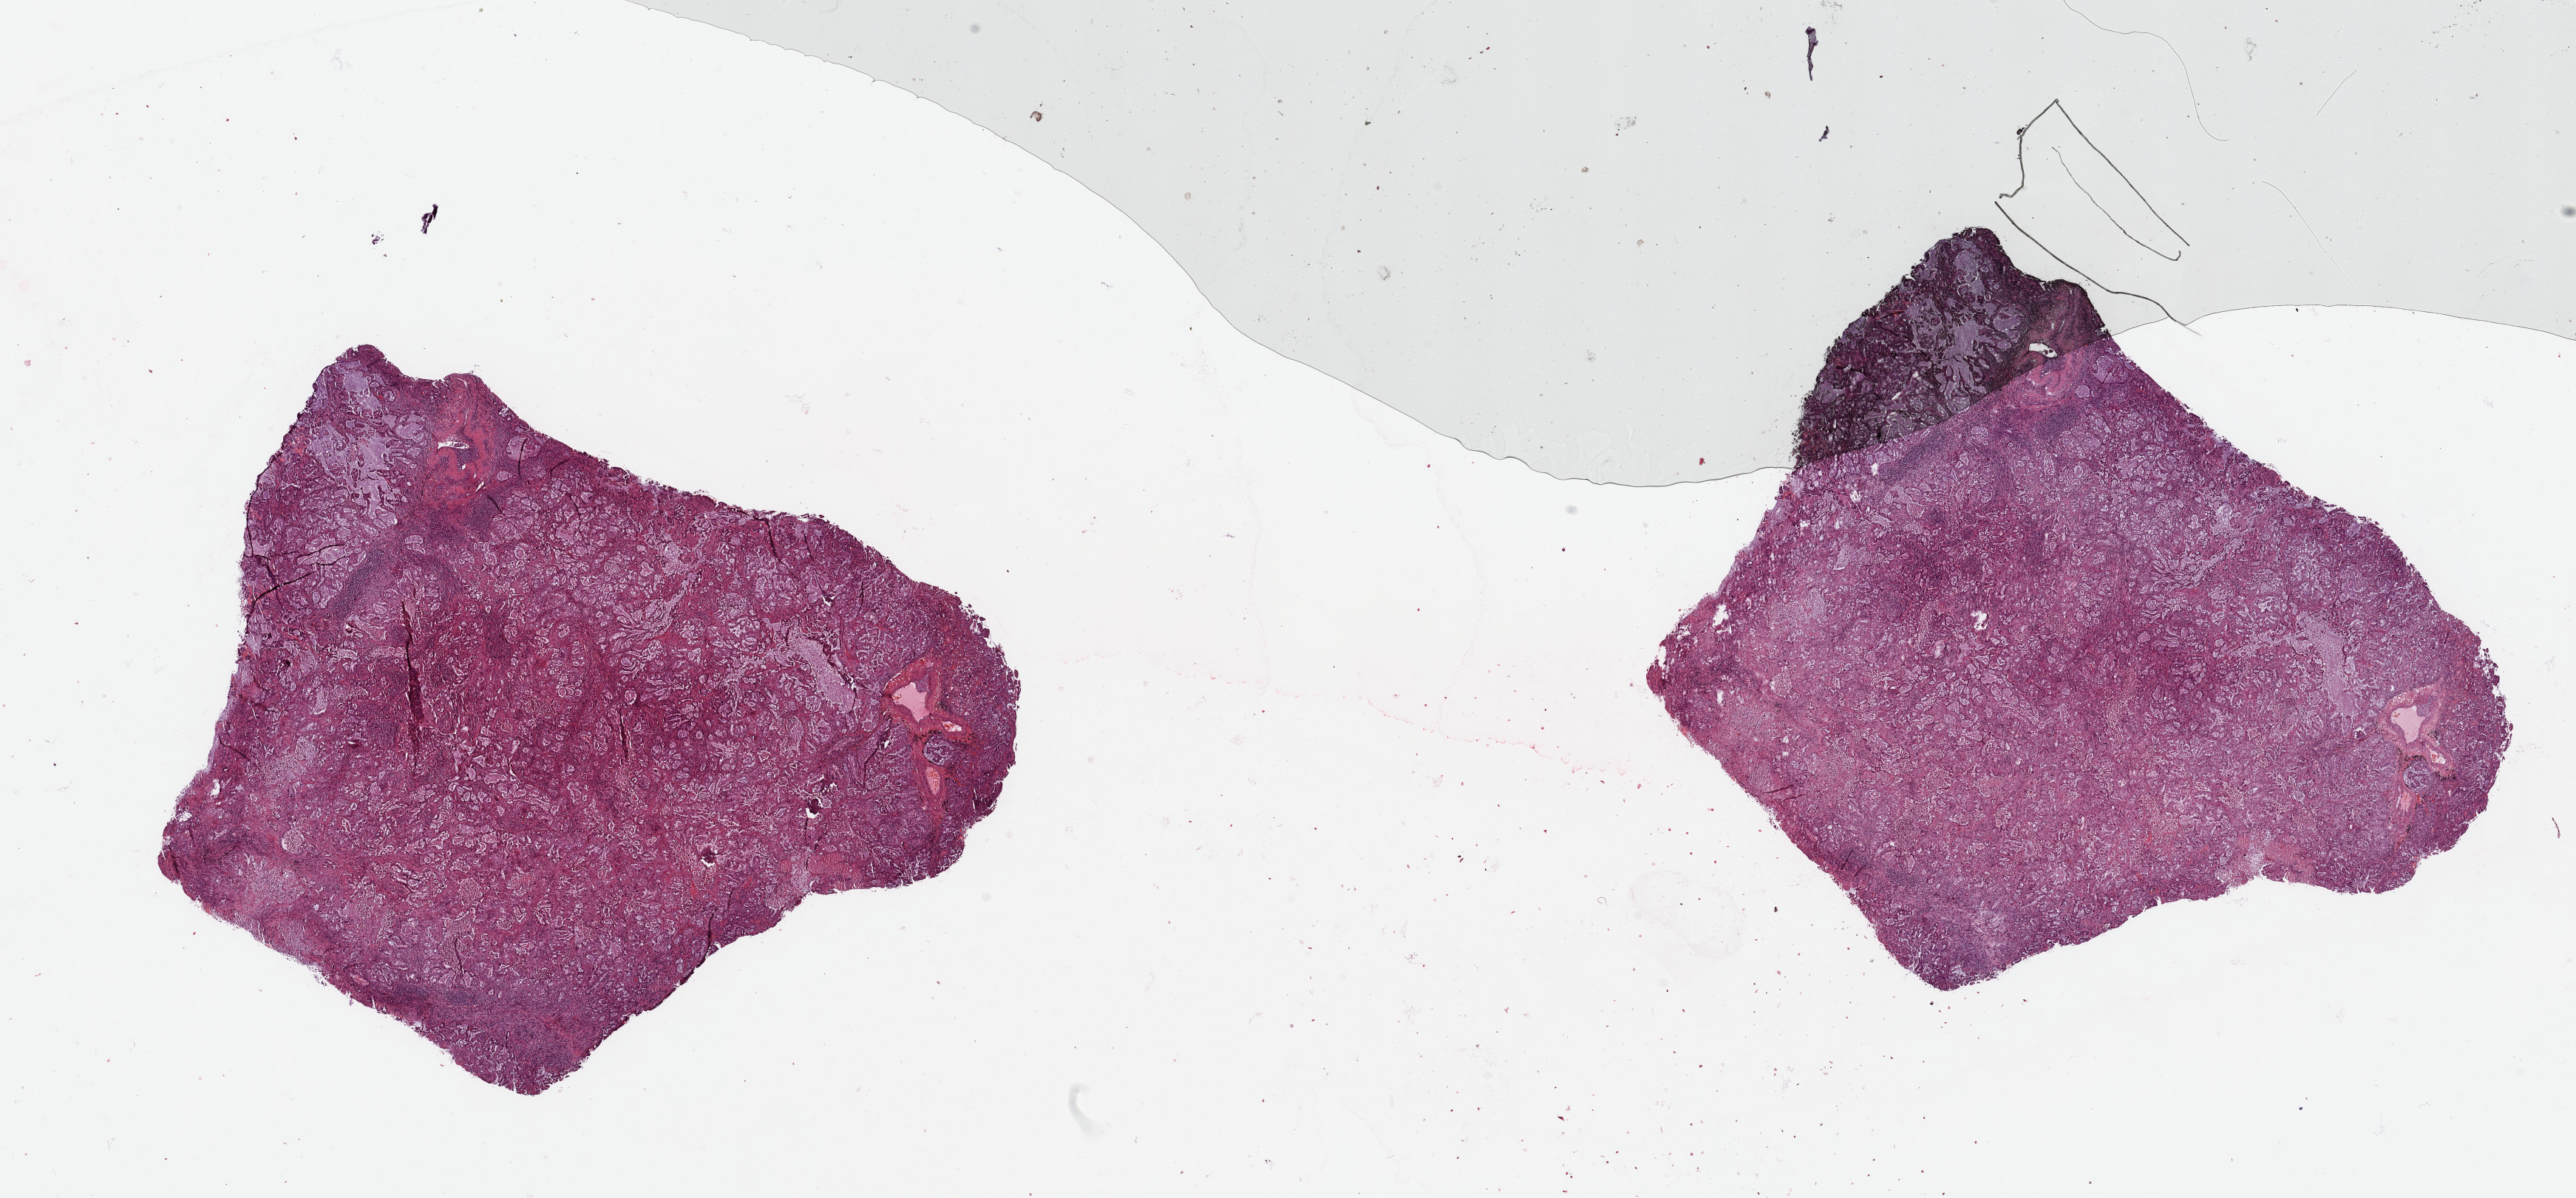
Digitized H&E-stained tissue section (whole slide), low-resolution overview of the scanned area, about 27.6 x 12.8 mm. Tumour tissue sample, lung. Patient: female, age 70 years. Histologic grade: G1 (well differentiated).
- AJCC pathologic stage: IIIA
- diagnosis: Adenocarcinoma, NOS